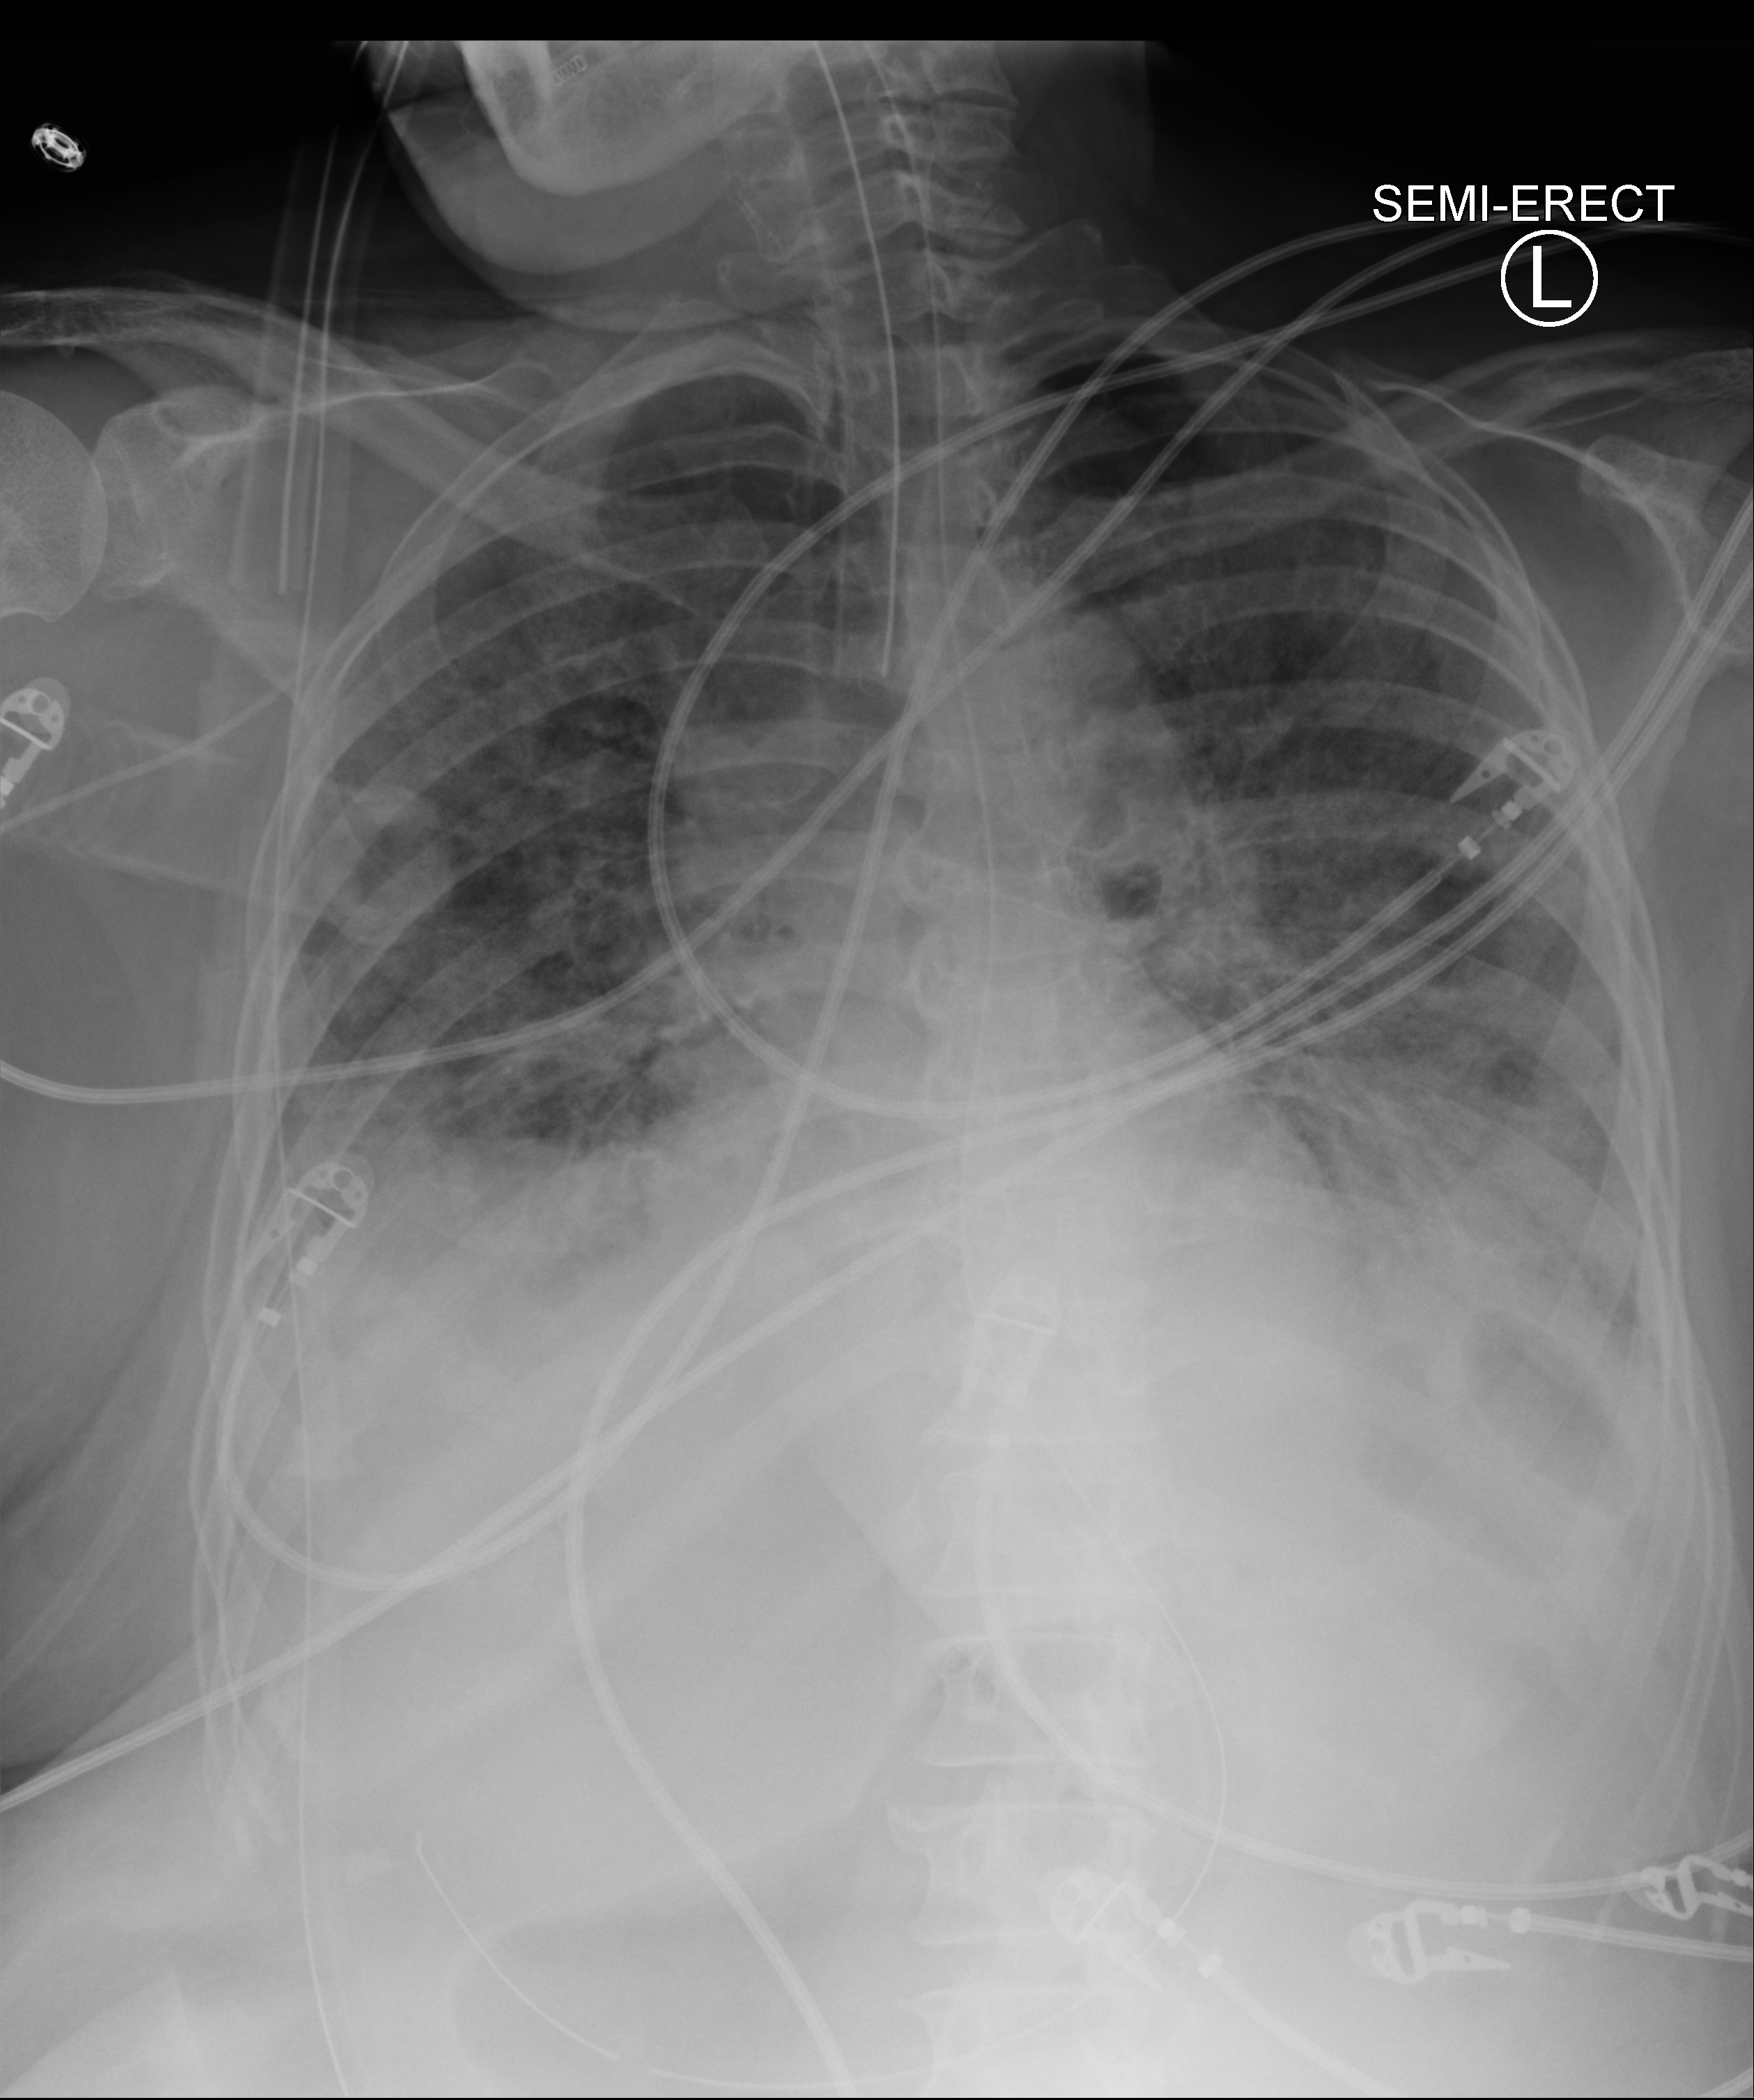
Bedside chest radiograph (computed radiography), anteroposterior (AP) projection. Patient hospitalised with COVID-19; female, aged 75–90 years.
From the hospital-stay record, not from the radiograph (when in the stay this image was taken is not recorded):
- admitted to intensive care during this hospital stay: yes